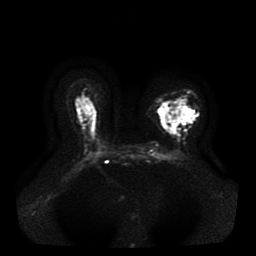
Breast MRI, one axial slice. Slice 26 of 41 in the series (ordered by position). Diffusion-weighted series; image 2 of 4 stored at this slice position (different b-values; order by instance number). 1.5 T. 256 × 256 image matrix, field of view 330 × 330 mm. Female patient.
Outlined on this slice (expert manual segmentation):
- tumour on diffusion-weighted imaging: bounding box [x1, y1, x2, y2] px = [158, 106, 193, 132]